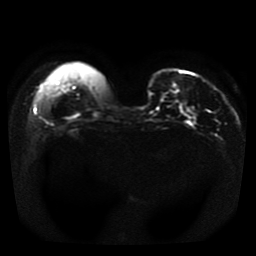
Breast MRI, one axial slice. Position 8 of 41 along the scan axis. Diffusion-weighted series; image 2 of 4 stored at this slice position (different b-values; order by instance number). 1.5 T. 5 mm slice thickness. 256 × 256 image matrix, field of view 330 × 330 mm. Female patient.
Outlined on this slice (manually delineated by an expert):
- tumour on diffusion-weighted imaging: box from (x=190, y=111) to (x=196, y=116) px